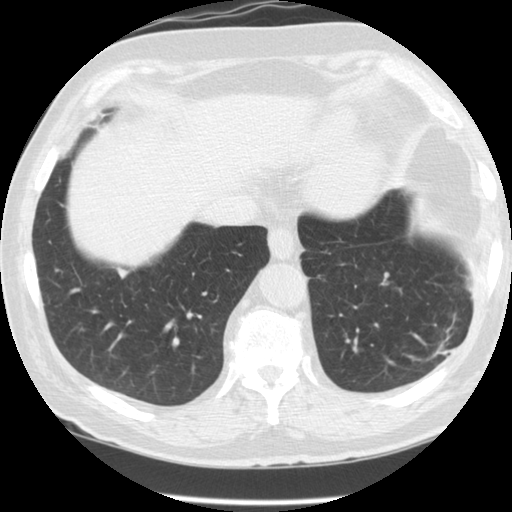
Low-dose screening chest CT, one axial slice; slice 35 of 127 in the series (ordered by position); lung window (W 1500 / L -600 HU); 2.5 mm slice thickness; 512 × 512 image matrix, field of view 340 × 340 mm.
Outlined on this slice (manually delineated by an expert):
- lesion 1 (tumor, lower lobe of left lung): box from (x=382, y=279) to (x=385, y=285) px